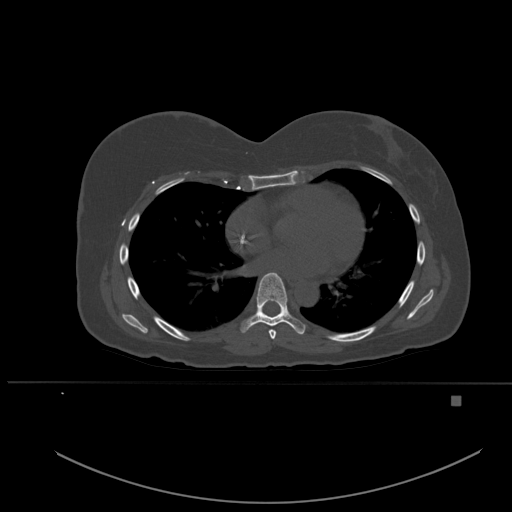
CT including the spine, one axial slice; position 337 of 651 along the scan axis; bone window (W 1800 / L 400 HU); 512 × 512 image matrix, field of view 443 × 443 mm. Female patient, age 49 years. From the clinical record (not read from this slice): primary cancer: breast; vertebrae with lytic lesions (as recorded): L3, T12, L4.
Outlined on this slice (semi-automatic segmentation, software-assisted and operator-edited):
- T6 vertebra: bounding box <269,330,277,339> (left, top, right, bottom; pixels)
- T7 vertebra: <241,272,305,335>